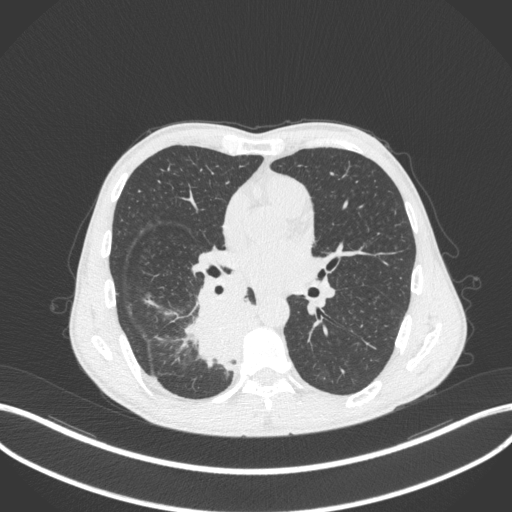
Chest CT, one axial slice. Position 192 of 371 along the scan axis. Reconstruction kernel B31f. 120 kVp. Lung window (W 1500 / L -600 HU). 1 mm slice thickness. 512 × 512 image matrix, field of view 400 × 400 mm. Male patient, age 58 years. From the clinical record (not read from this slice): clinical TNM (as recorded): T3 N1 M1.
Annotated regions visible in this slice (bounding box drawn by a radiologist):
- lung tumour (recorded histology: squamous cell carcinoma): bounding box <184,289,264,372> (left, top, right, bottom; pixels)